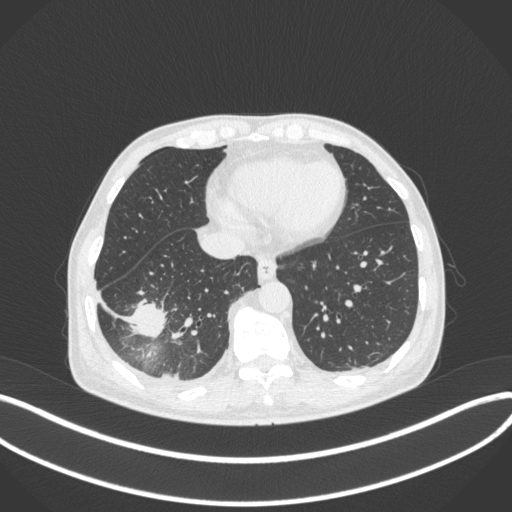
Chest CT, one axial slice. Reconstruction kernel B31f. 120 kVp. Lung window (W 1500 / L -600 HU). 512 × 512 image matrix, field of view 400 × 400 mm. Male patient, age 64 years. From the clinical record (not read from this slice): clinical TNM (as recorded): T3 N0 M0; histopathological grade: G2-3.
Annotated regions visible in this slice (bounding box drawn by a radiologist):
- lung tumour (recorded histology: adenocarcinoma): bounding box (x1, y1, x2, y2) in pixels: (126, 296, 169, 339)